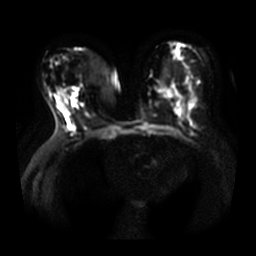
Breast MRI, one axial slice; slice 16 of 33 in the series (ordered by position); diffusion-weighted series; image 2 of 4 stored at this slice position (different b-values; order by instance number); 3 T; 5 mm slice thickness; 256 × 256 image matrix, field of view 360 × 360 mm. Female patient.
Annotated regions visible in this slice (outlined manually by an expert reader):
- tumour on diffusion-weighted imaging: box from (x=72, y=88) to (x=79, y=96) px